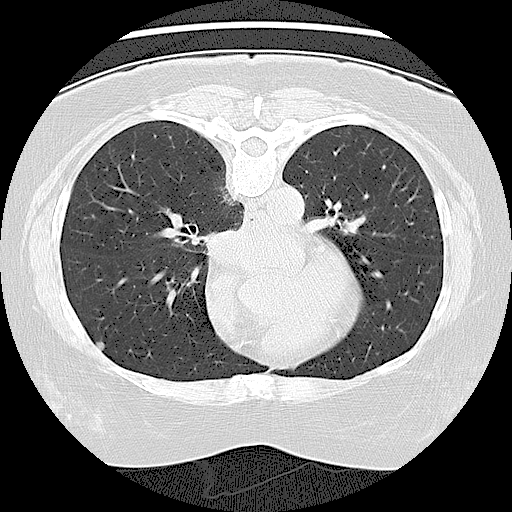
Chest CT (low-dose screening protocol), one axial image, baseline annual screen, lung window (W 1500 / L -600 HU), 2.5 mm slice thickness, lung (sharp) reconstruction kernel (LUNG), slice 62 of 108 in the series. Female, age 67 years at enrolment. Former smoker at enrolment.
Expert-annotated lung lesion, bounding box <79,328,122,369> (left, top, right, bottom; pixels). The exam's reader record, not a measurement of the box and not confirmed to be the same lesion: non-calcified nodule or mass ≥4 mm, right middle lobe, 5 × 5 mm, smooth margins, soft tissue attenuation.